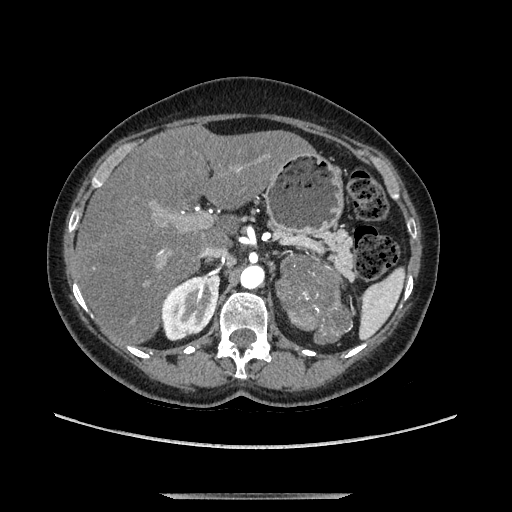
Contrast-enhanced abdominal CT, one axial slice. Position 79 of 169 along the scan axis. Soft-tissue window (W 400 / L 40 HU). 1.25 mm slice thickness. 512 × 512 image matrix. Female patient. Case-level facts recorded for this patient, not image findings: diagnosis: adrenocortical carcinoma; tumour side: left adrenal.
Outlined on this slice (semi-automatically segmented with operator editing):
- mass: bounding box [x1, y1, x2, y2] px = [279, 260, 348, 340]